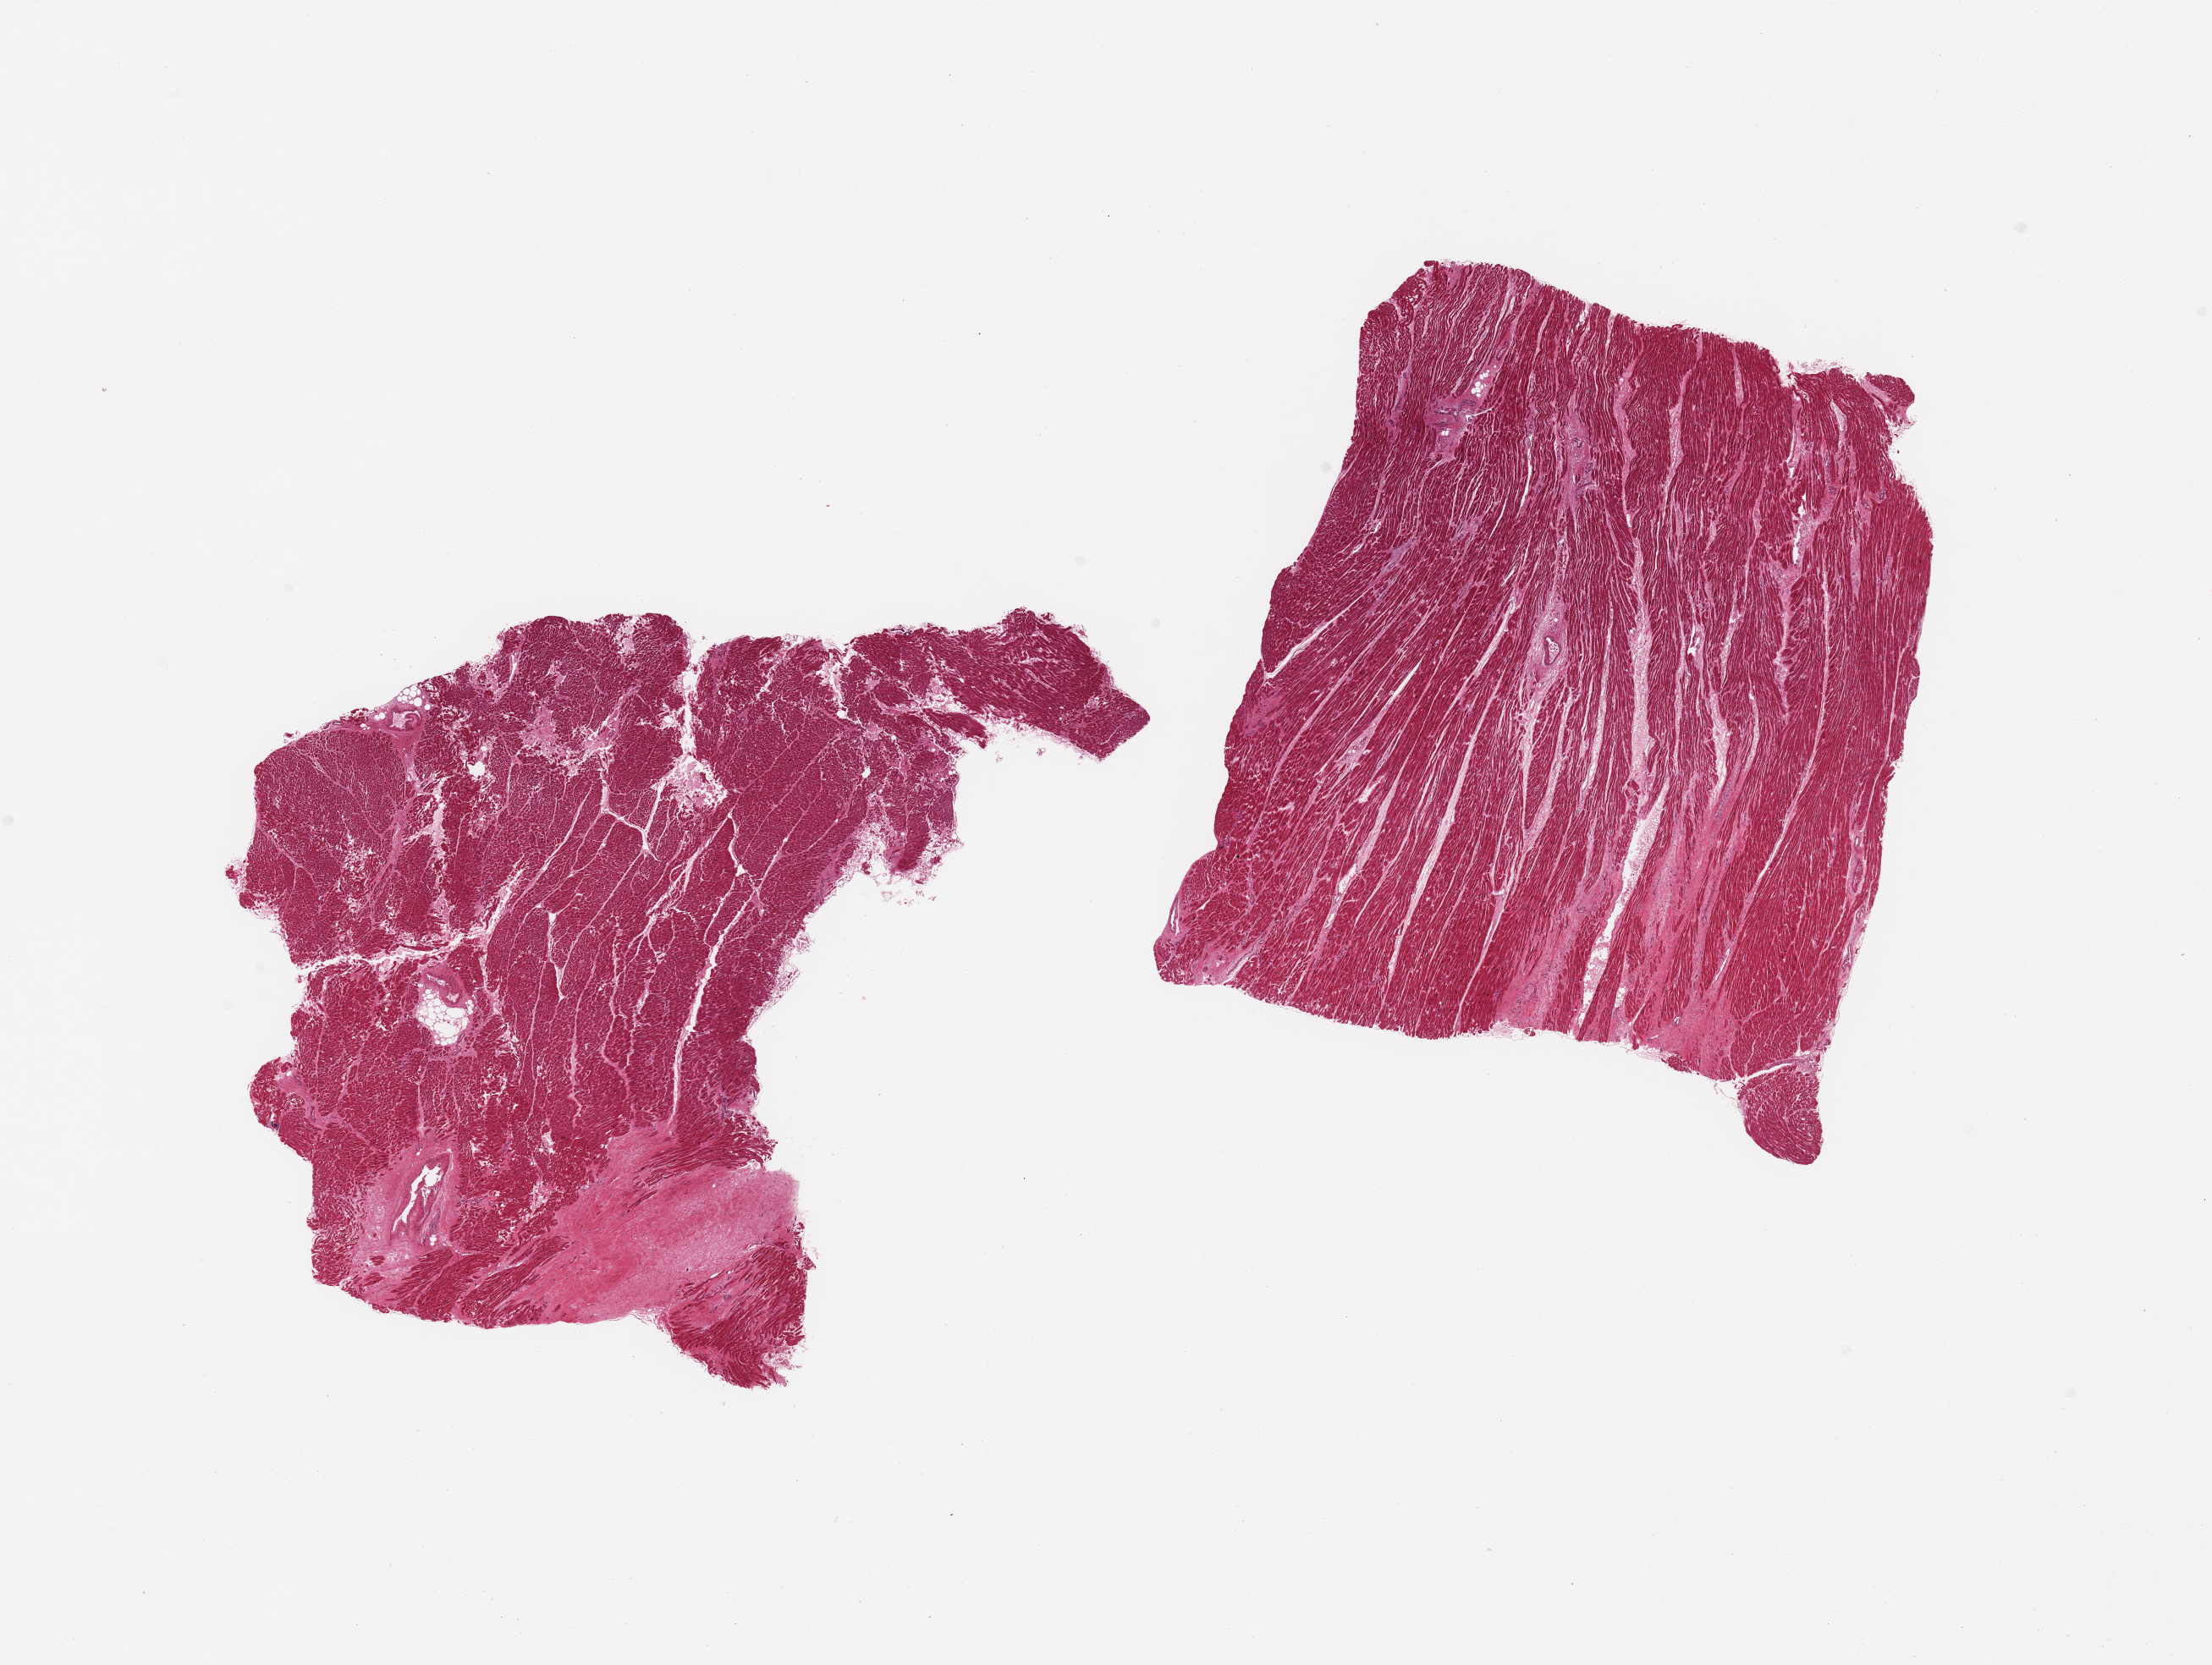
Whole-slide image, hematoxylin and eosin (H&E) stain — shown as a low-resolution overview of the whole scanned area (about 20.7 x 15.6 mm). PAXgene-fixed paraffin-embedded (PFPE) section. Sampled site (target tissue): heart. Tissue donor sample. Donor sex: male.
- pathologist's review note for this sample: 2 pieces; scars consistent with old infarcts, largest 2.7 mm across